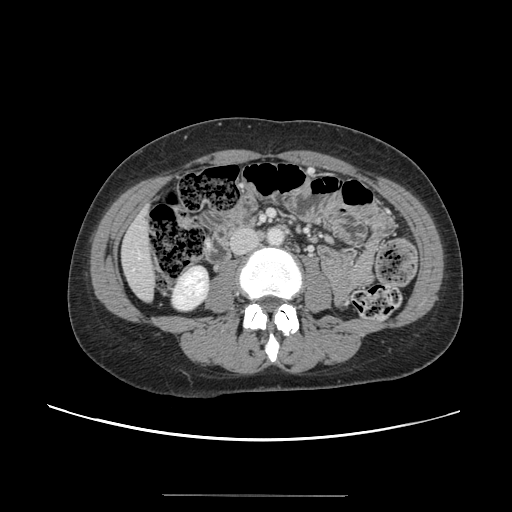
Contrast-enhanced abdominal CT, one axial slice. Slice 27 of 144 in the series (ordered by position). 120 kVp. Soft-tissue window (W 400 / L 40 HU). 2.5 mm slice thickness. 512 × 512 image matrix, field of view 380 × 380 mm. Female patient, age 53 years. Case-level facts recorded for this patient, not image findings: diagnosis: colorectal cancer liver metastases, imaged before liver resection; multiple liver metastases: yes; largest metastasis: 1.1 cm; chemotherapy before resection: no.
Structures marked on this image (outlined manually by an expert reader):
- liver: bounding box [x1, y1, x2, y2] px = [123, 210, 155, 300]
- planned liver remnant (the part of the liver to remain after resection): [122, 210, 155, 300]